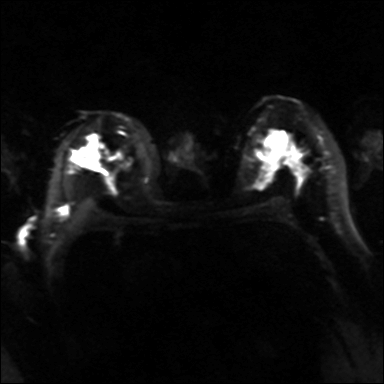
Breast MRI, one axial slice. Slice 21 of 36 in the series (ordered by position). Diffusion-weighted series; image 2 of 4 stored at this slice position (different b-values; order by instance number). 3 T. 4 mm slice thickness. 384 × 384 image matrix, field of view 320 × 320 mm. Female patient.
Structures marked on this image (manually delineated by an expert):
- tumour on diffusion-weighted imaging: bounding box (x1, y1, x2, y2) in pixels: (76, 142, 98, 168)